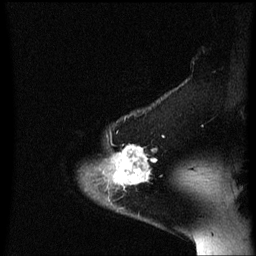
Breast MRI (dynamic contrast-enhanced), one sagittal slice. Slice 52 of 60 in the series (ordered by position). Dynamic contrast-enhanced series, image 2 of 3 at this slice position (ordered by acquisition). 1.5 T. TE 4.2 ms, TR 8.4 ms. 2 mm slice thickness. 256 × 256 image matrix, field of view 200 × 200 mm. Female patient, age 54 years. Case-level facts recorded for this patient, not image findings: setting: breast cancer imaged before/during neoadjuvant chemotherapy; receptor status: HR-positive, HER2-negative.
Structures marked on this image (semi-automatic segmentation, software-assisted and operator-edited):
- analysis volume of interest (the breast-tissue region the enhancement analysis was run in; not a lesion): bounding box <102,134,160,199> (left, top, right, bottom; pixels)
- tumour enhancement mask (voxels above the 70 % enhancement threshold inside the analysis volume of interest): <104,146,158,189>